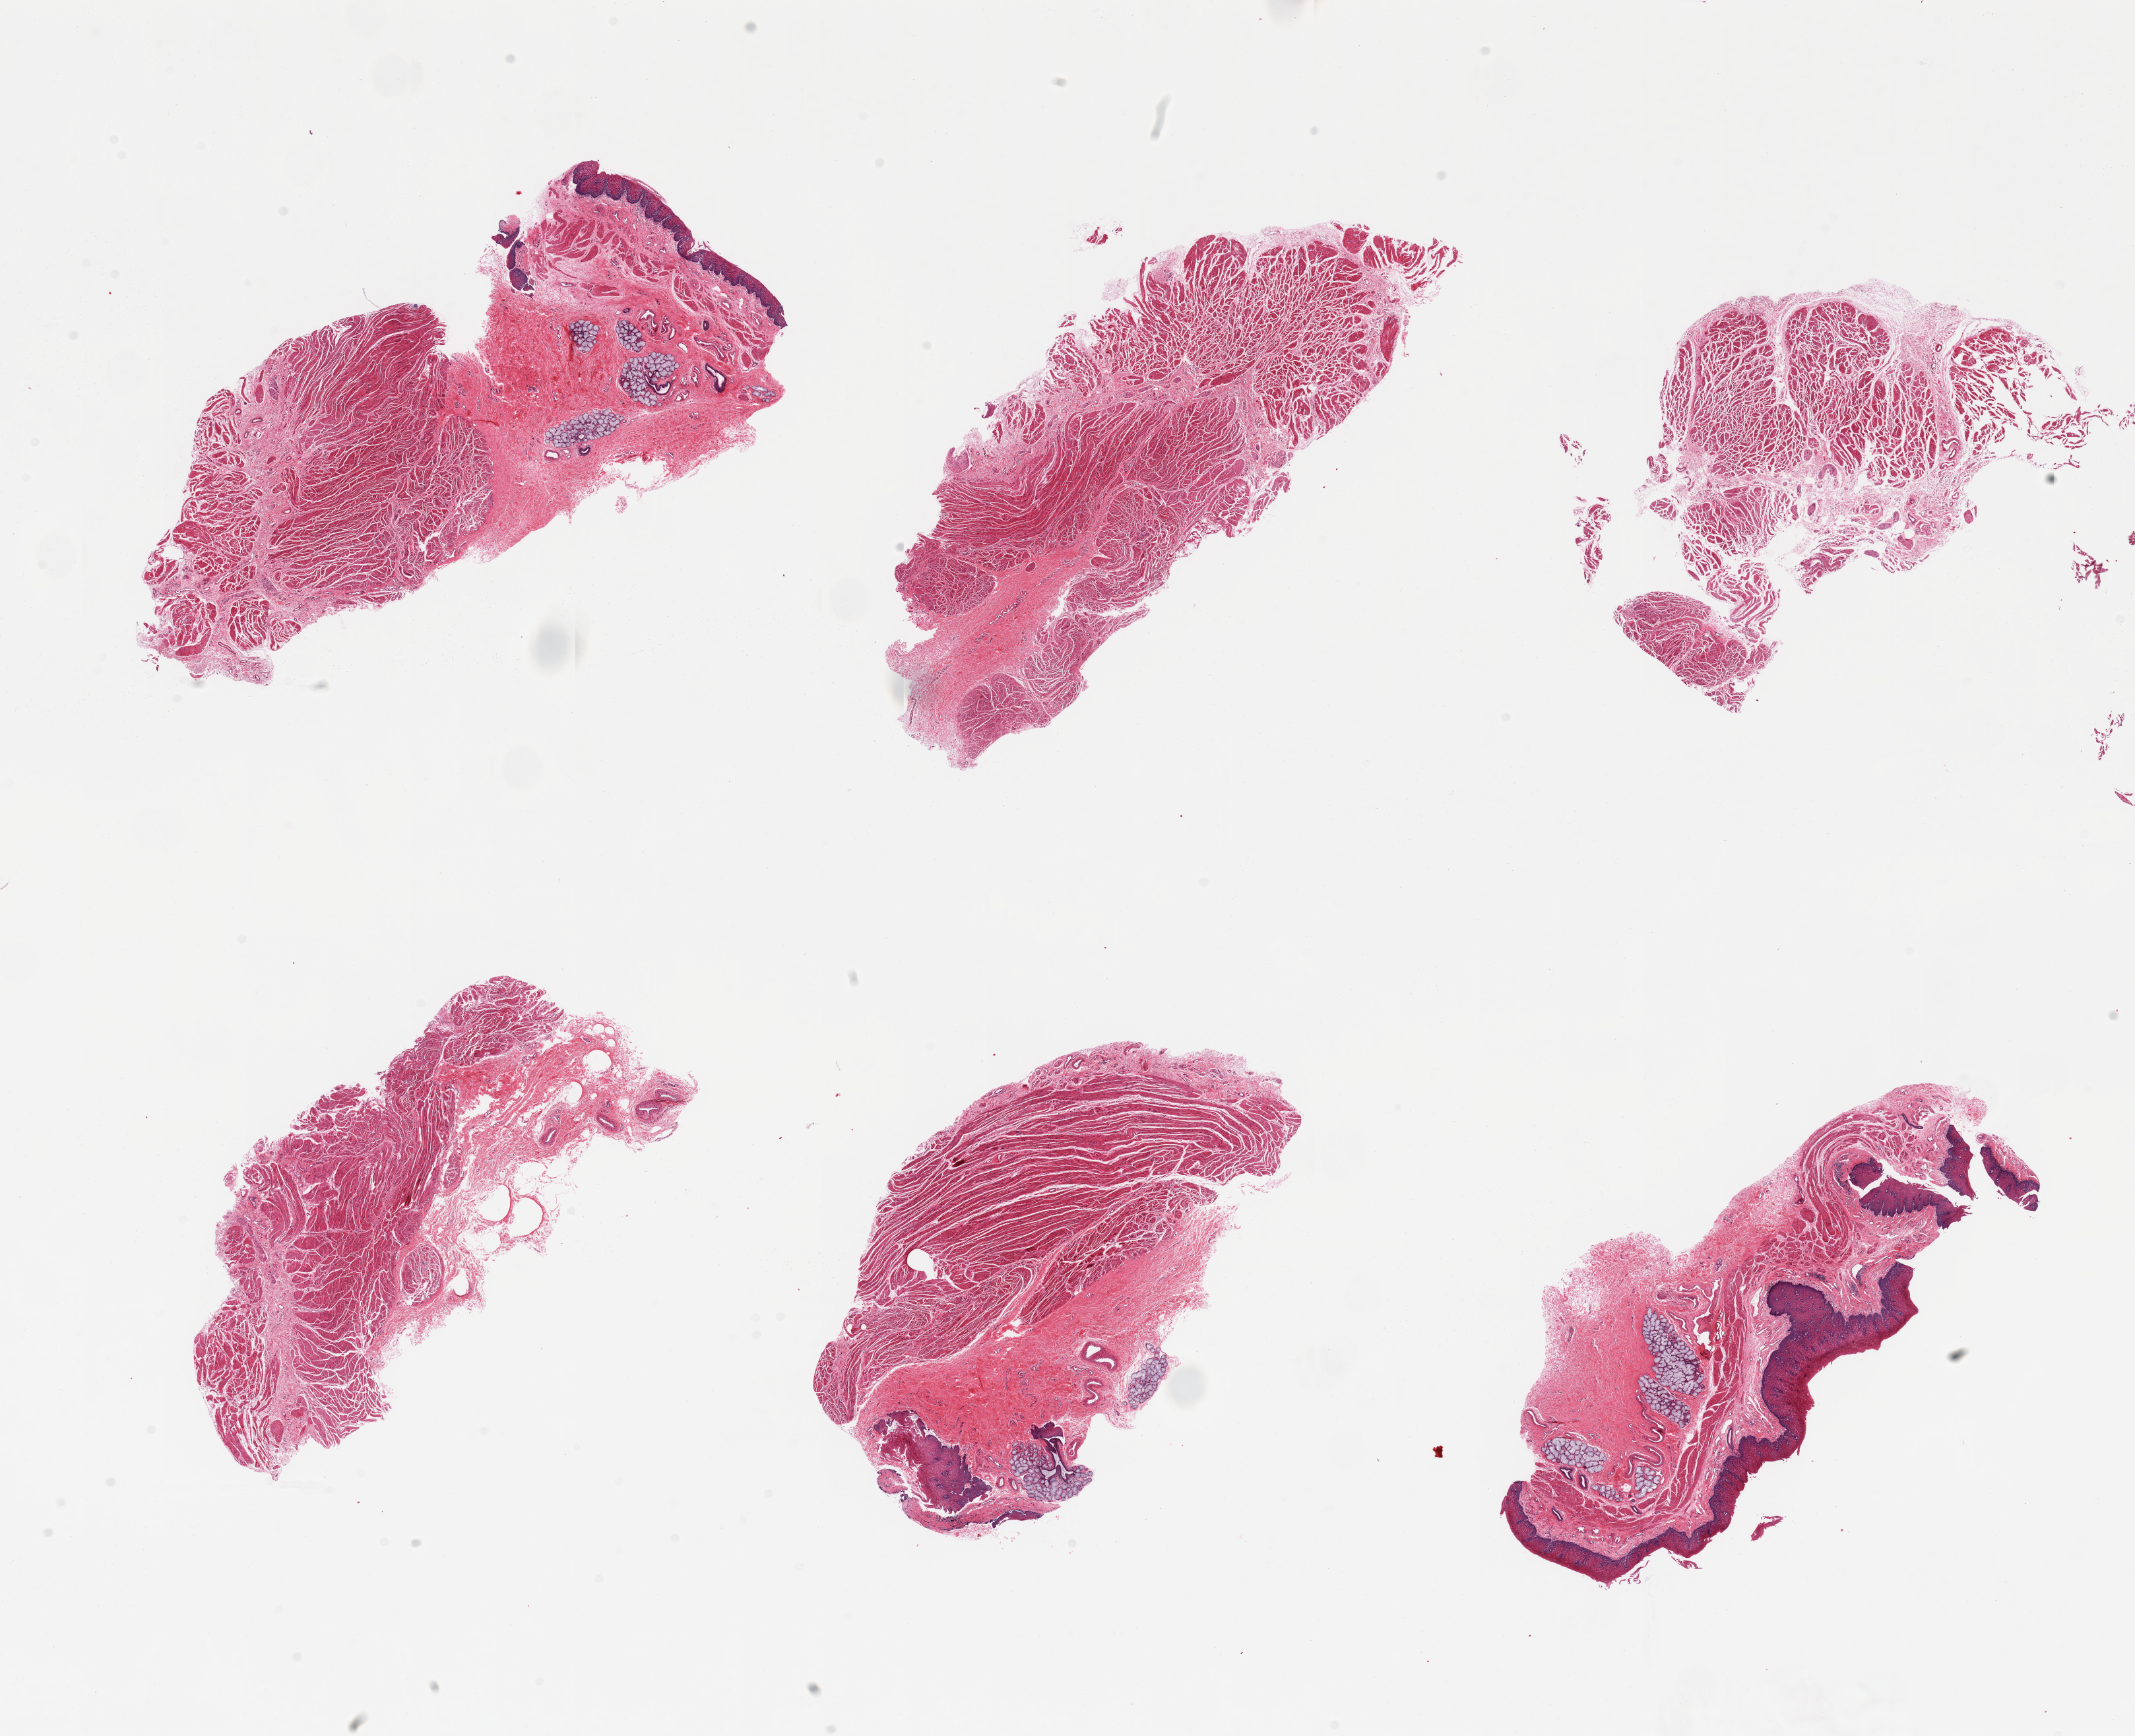
Digitized H&E-stained section, whole scanned area (about 25.6 x 20.8 mm, acquisition: 20x scan) shown as a low-resolution overview; PAXgene-fixed, paraffin-embedded tissue; sampled site (target tissue): esophageal mucous membrane; tissue donor sample. Male donor.
Reviewer comment on this tissue sample: 6 pieces, mucosa and muscularis, 2 with sufficient squamous epithelium; others may have epithelium deeper in blocks.